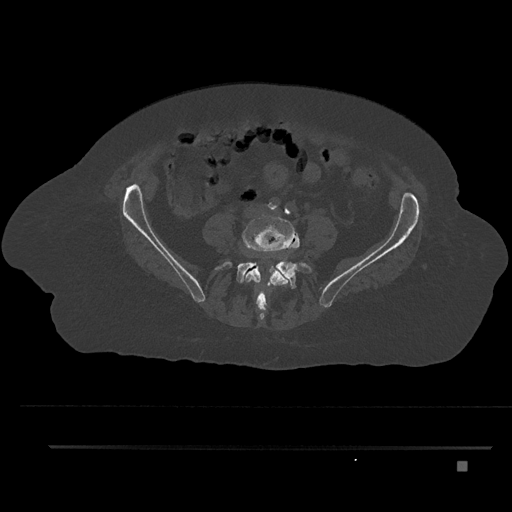
CT including the spine, one axial slice; slice 58 of 797 in the series (ordered by position); 120 kVp; bone window (W 1800 / L 400 HU); 0.5 mm slice thickness; 512 × 512 image matrix, field of view 437 × 437 mm. Patient: female, 76 years. From the clinical record (not read from this slice): primary cancer: lung; vertebrae with lytic lesions (as recorded): T11, L3.
Annotated regions visible in this slice (semi-automatic segmentation, software-assisted and operator-edited):
- L4 vertebra: bounding box <243,216,299,314> (left, top, right, bottom; pixels)
- L5 vertebra: <215,262,312,320>